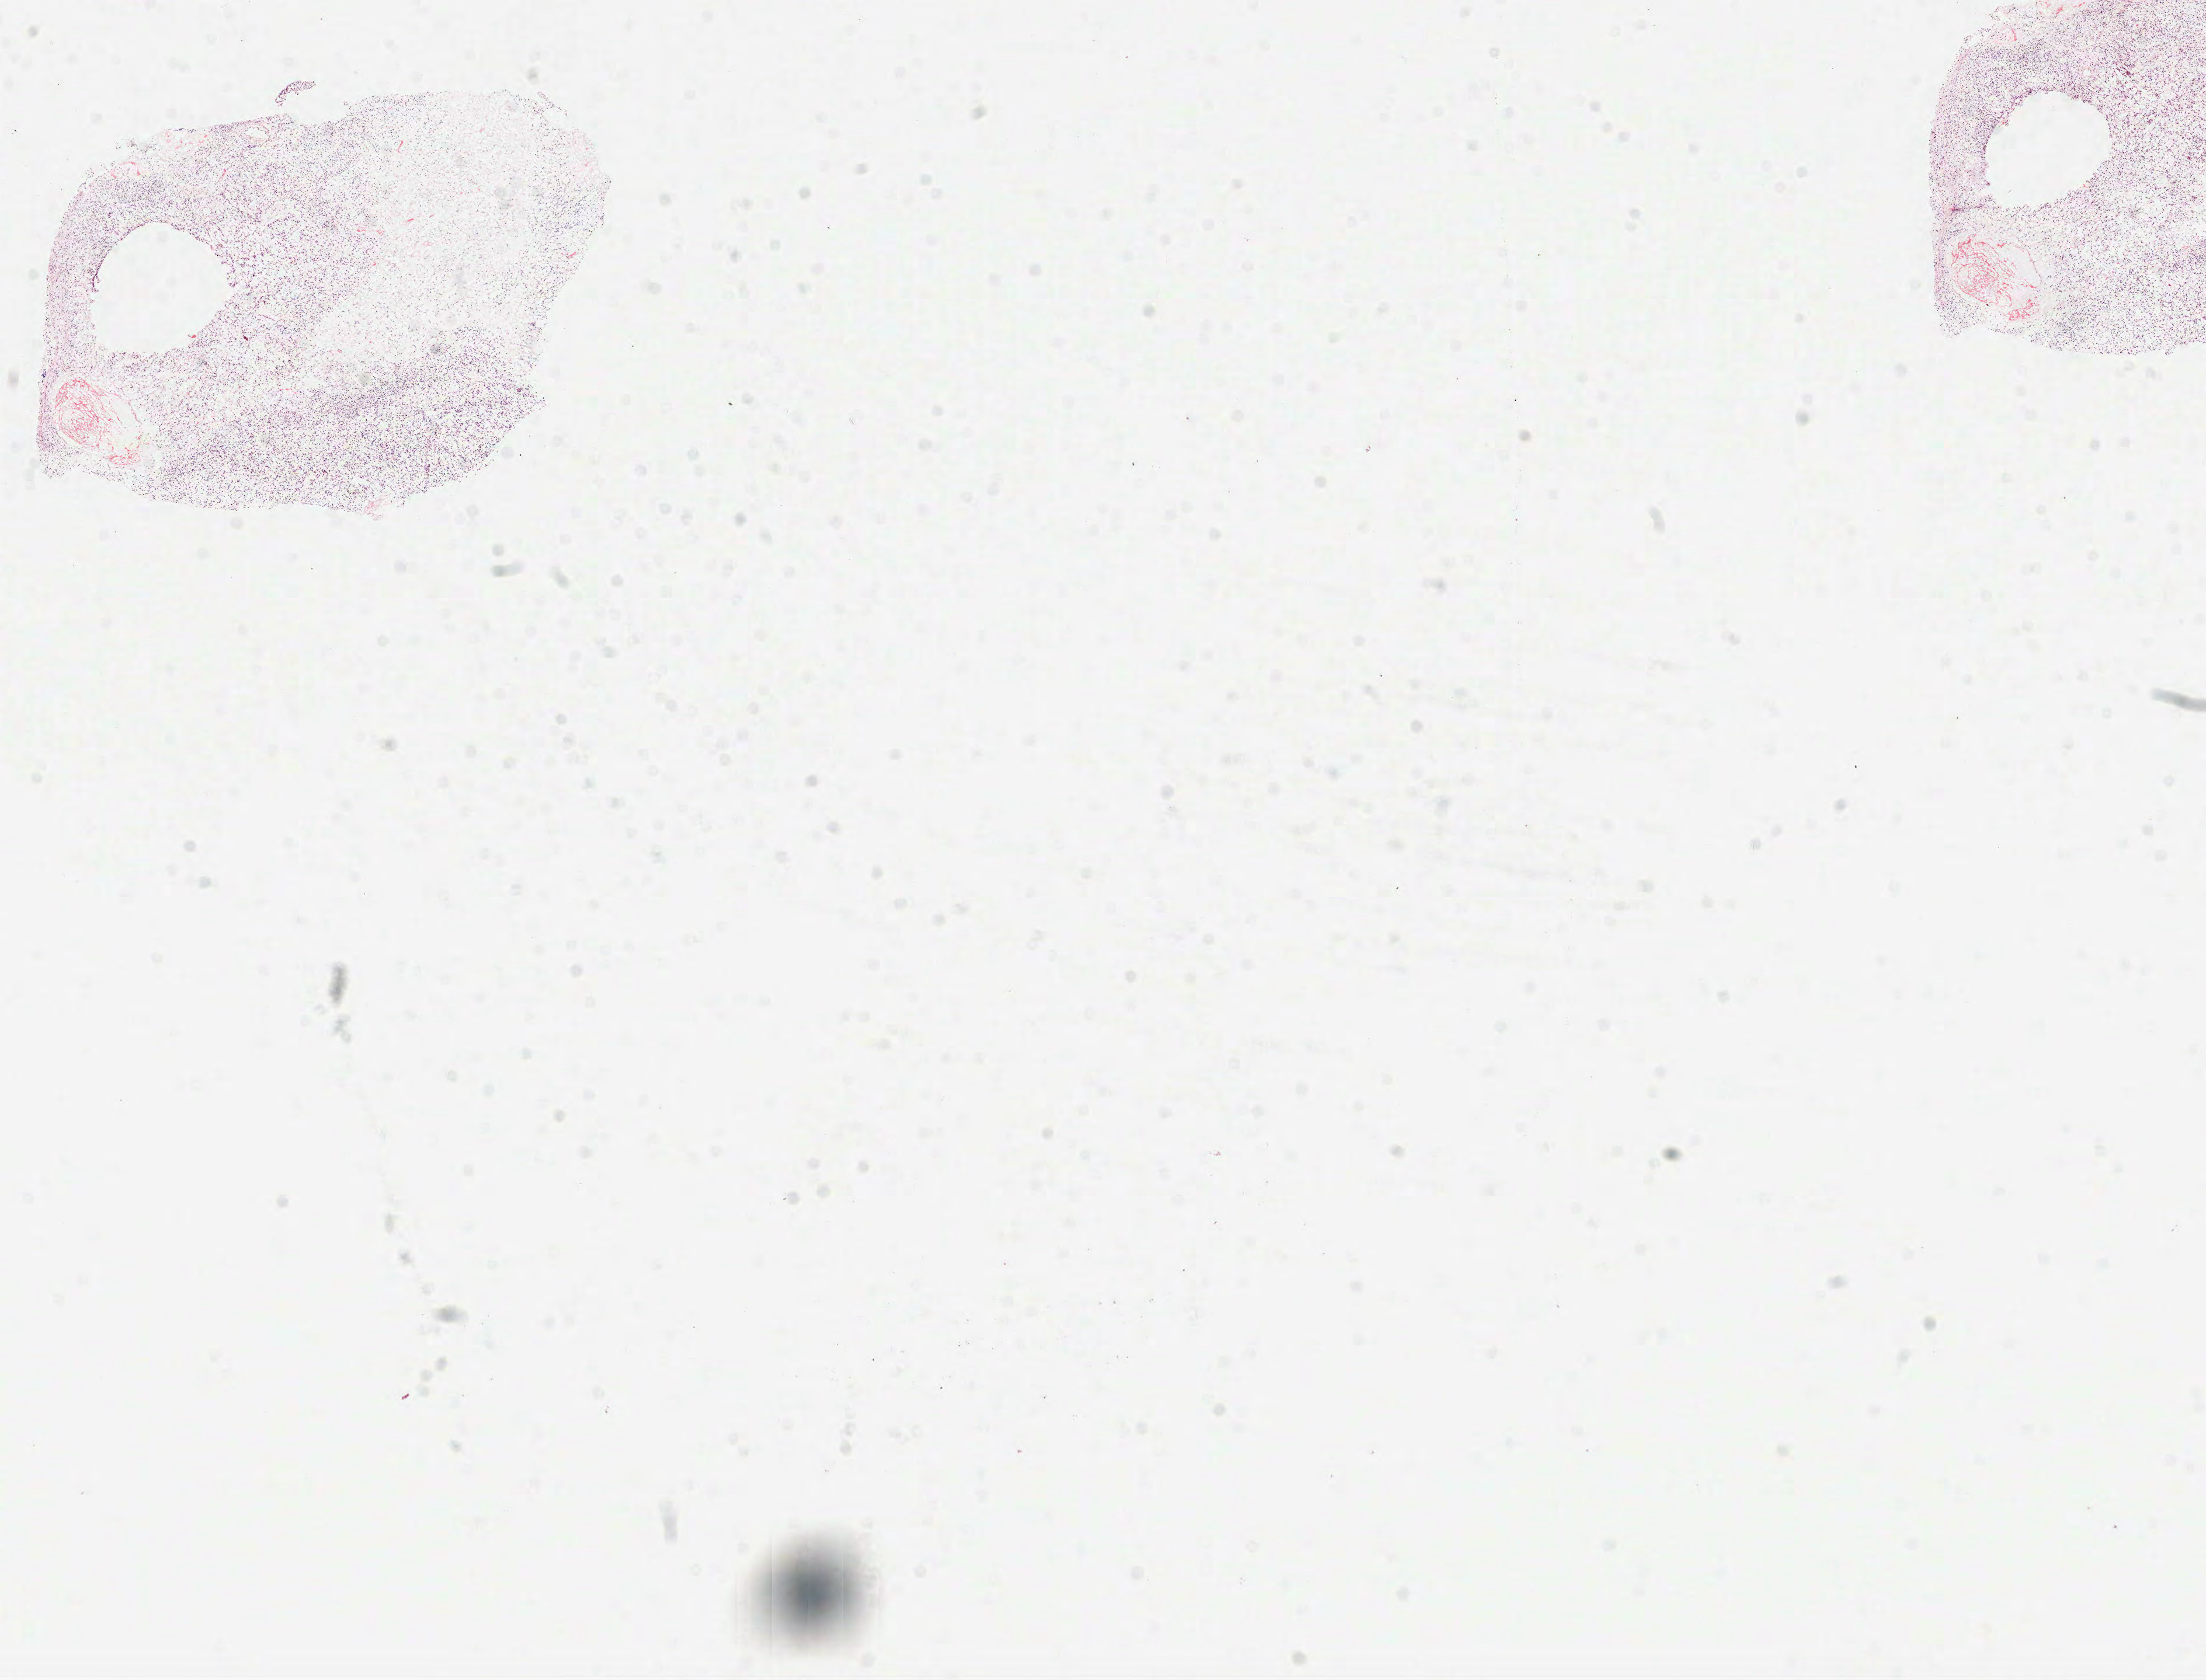
Hematoxylin and eosin (H&E) stained whole-slide image, whole scanned area (about 15.2 x 11.6 mm) shown as a low-resolution overview, formalin-fixed paraffin-embedded (FFPE) diagnostic section, sample: primary tumour, brain. Female, age 64 years at initial diagnosis.
Pathologic diagnosis: Glioblastoma.